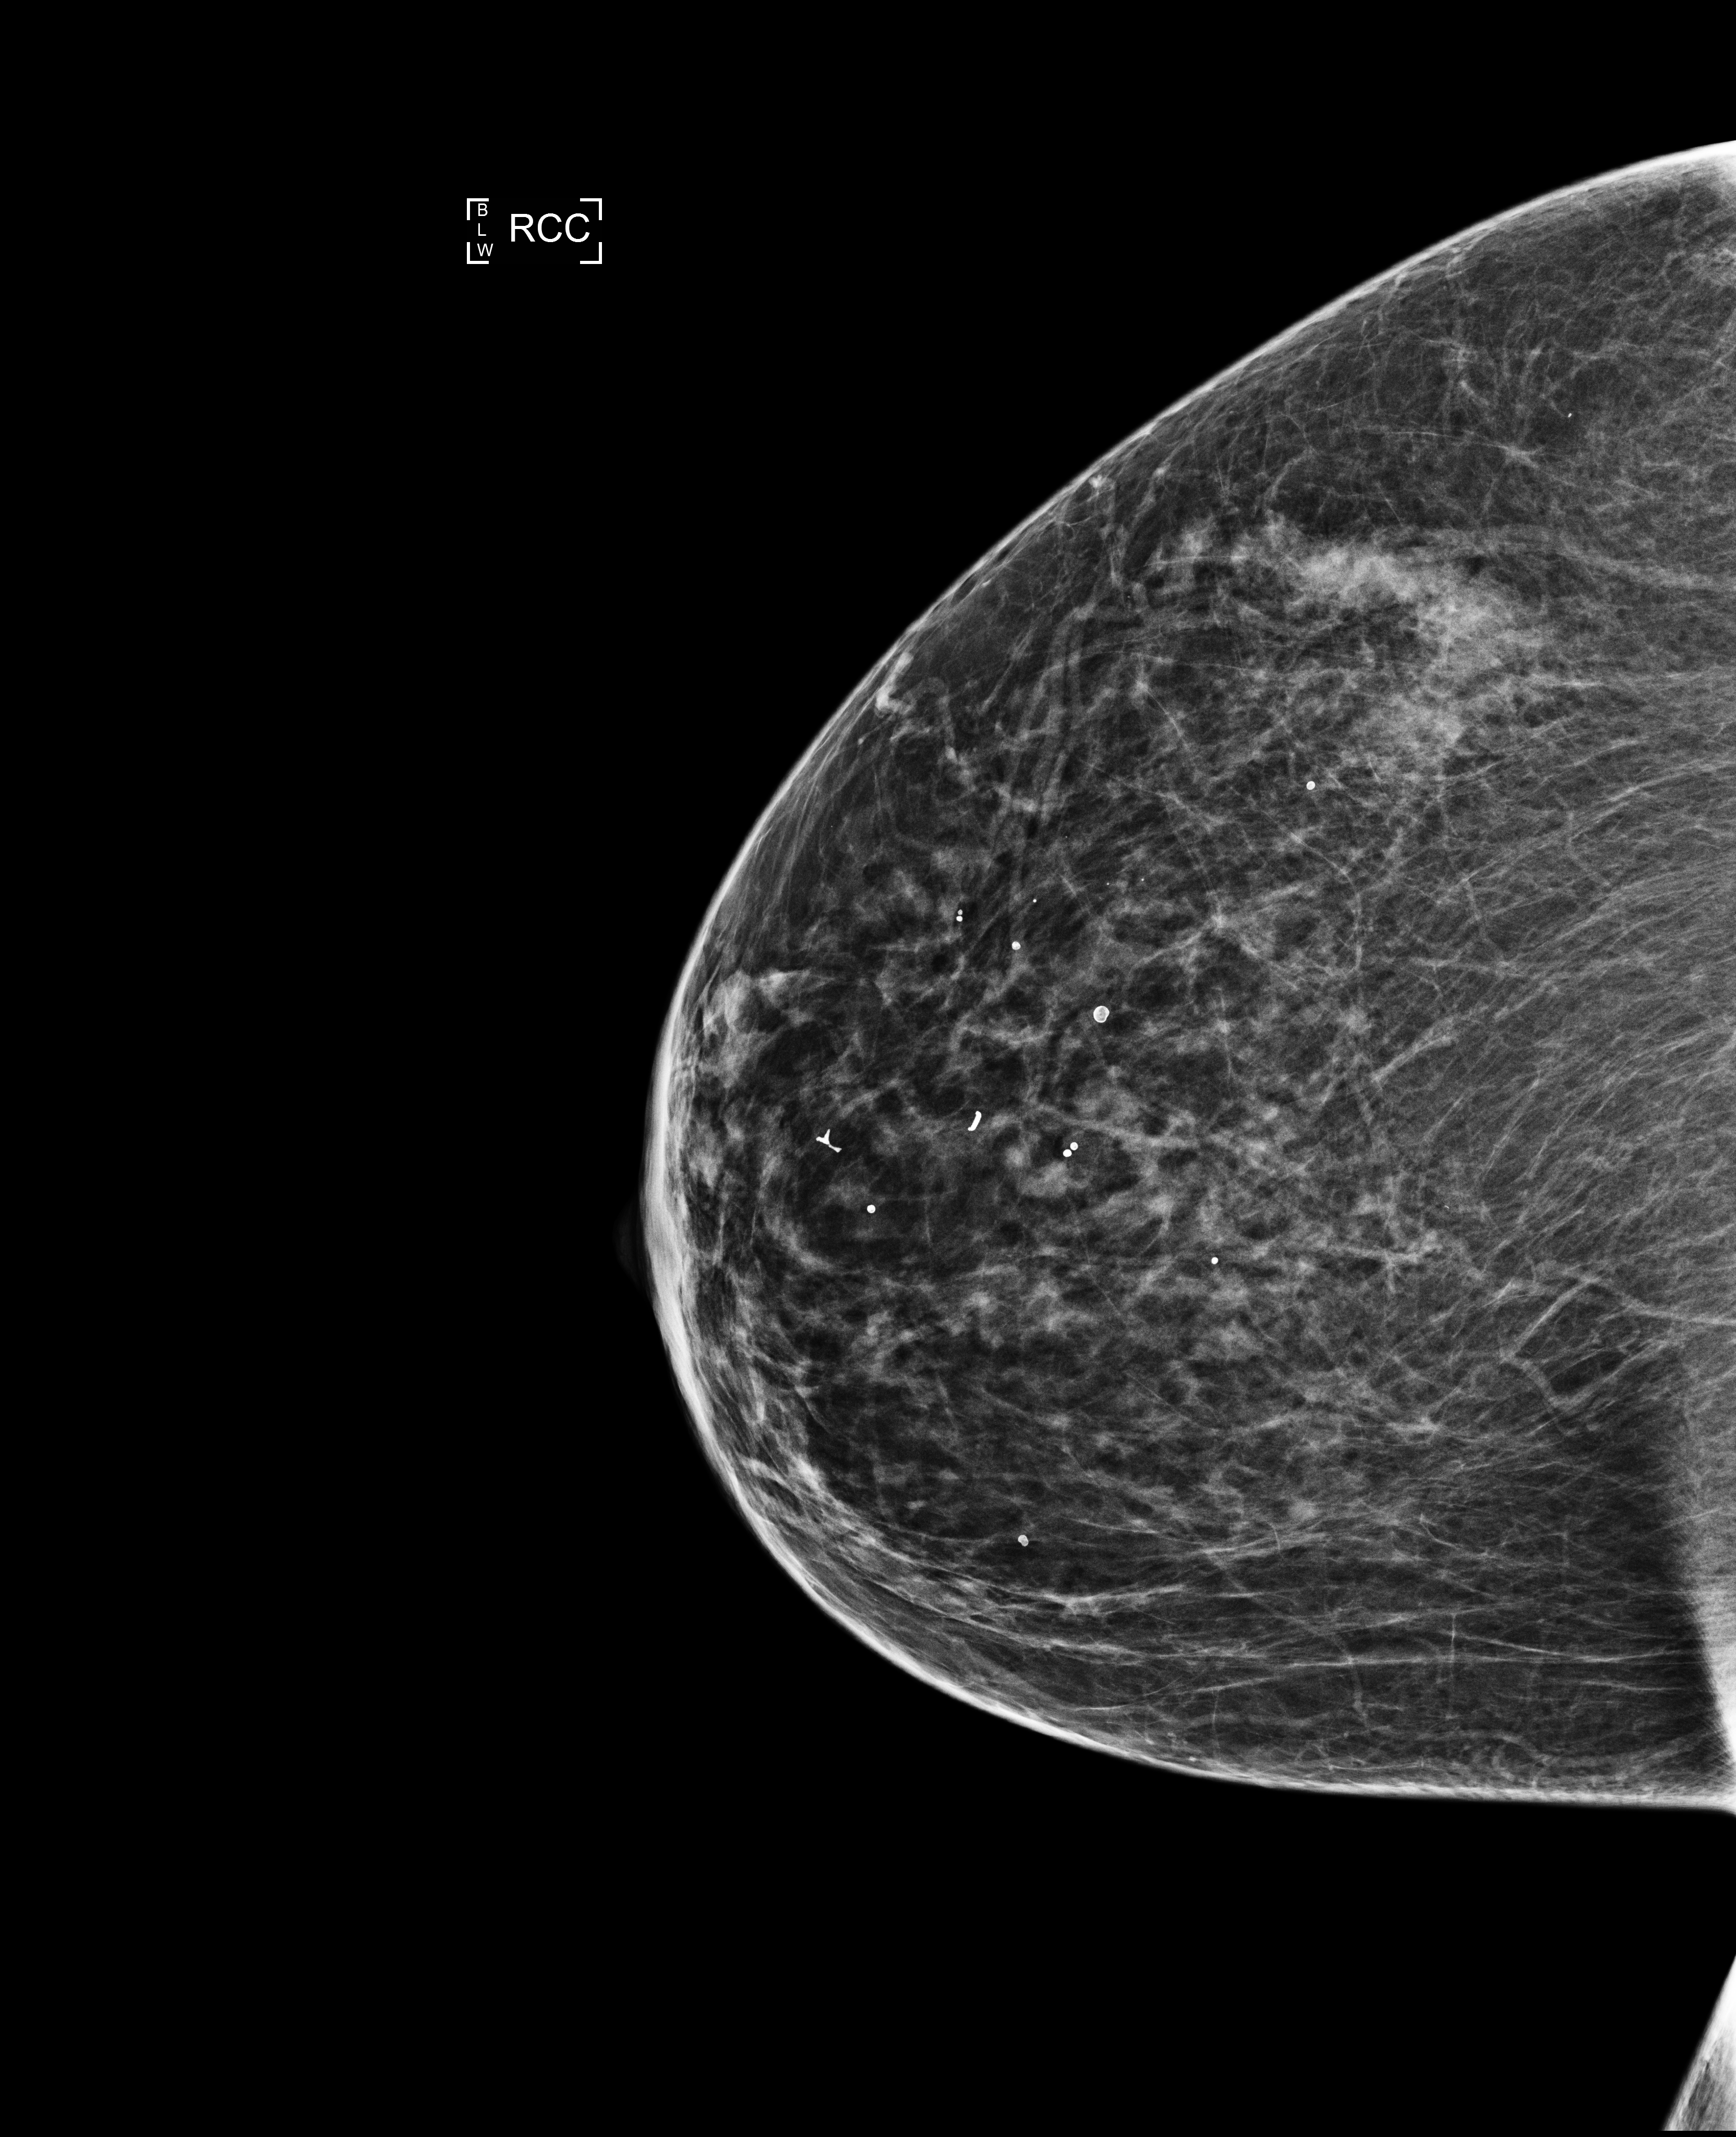
Screening examination, compressed breast thickness 39 mm, system: Selenia Dimensions. Patient: female, 69 years.
Image type: full-field digital mammogram. Breast: right. Projection: cranio-caudal projection.